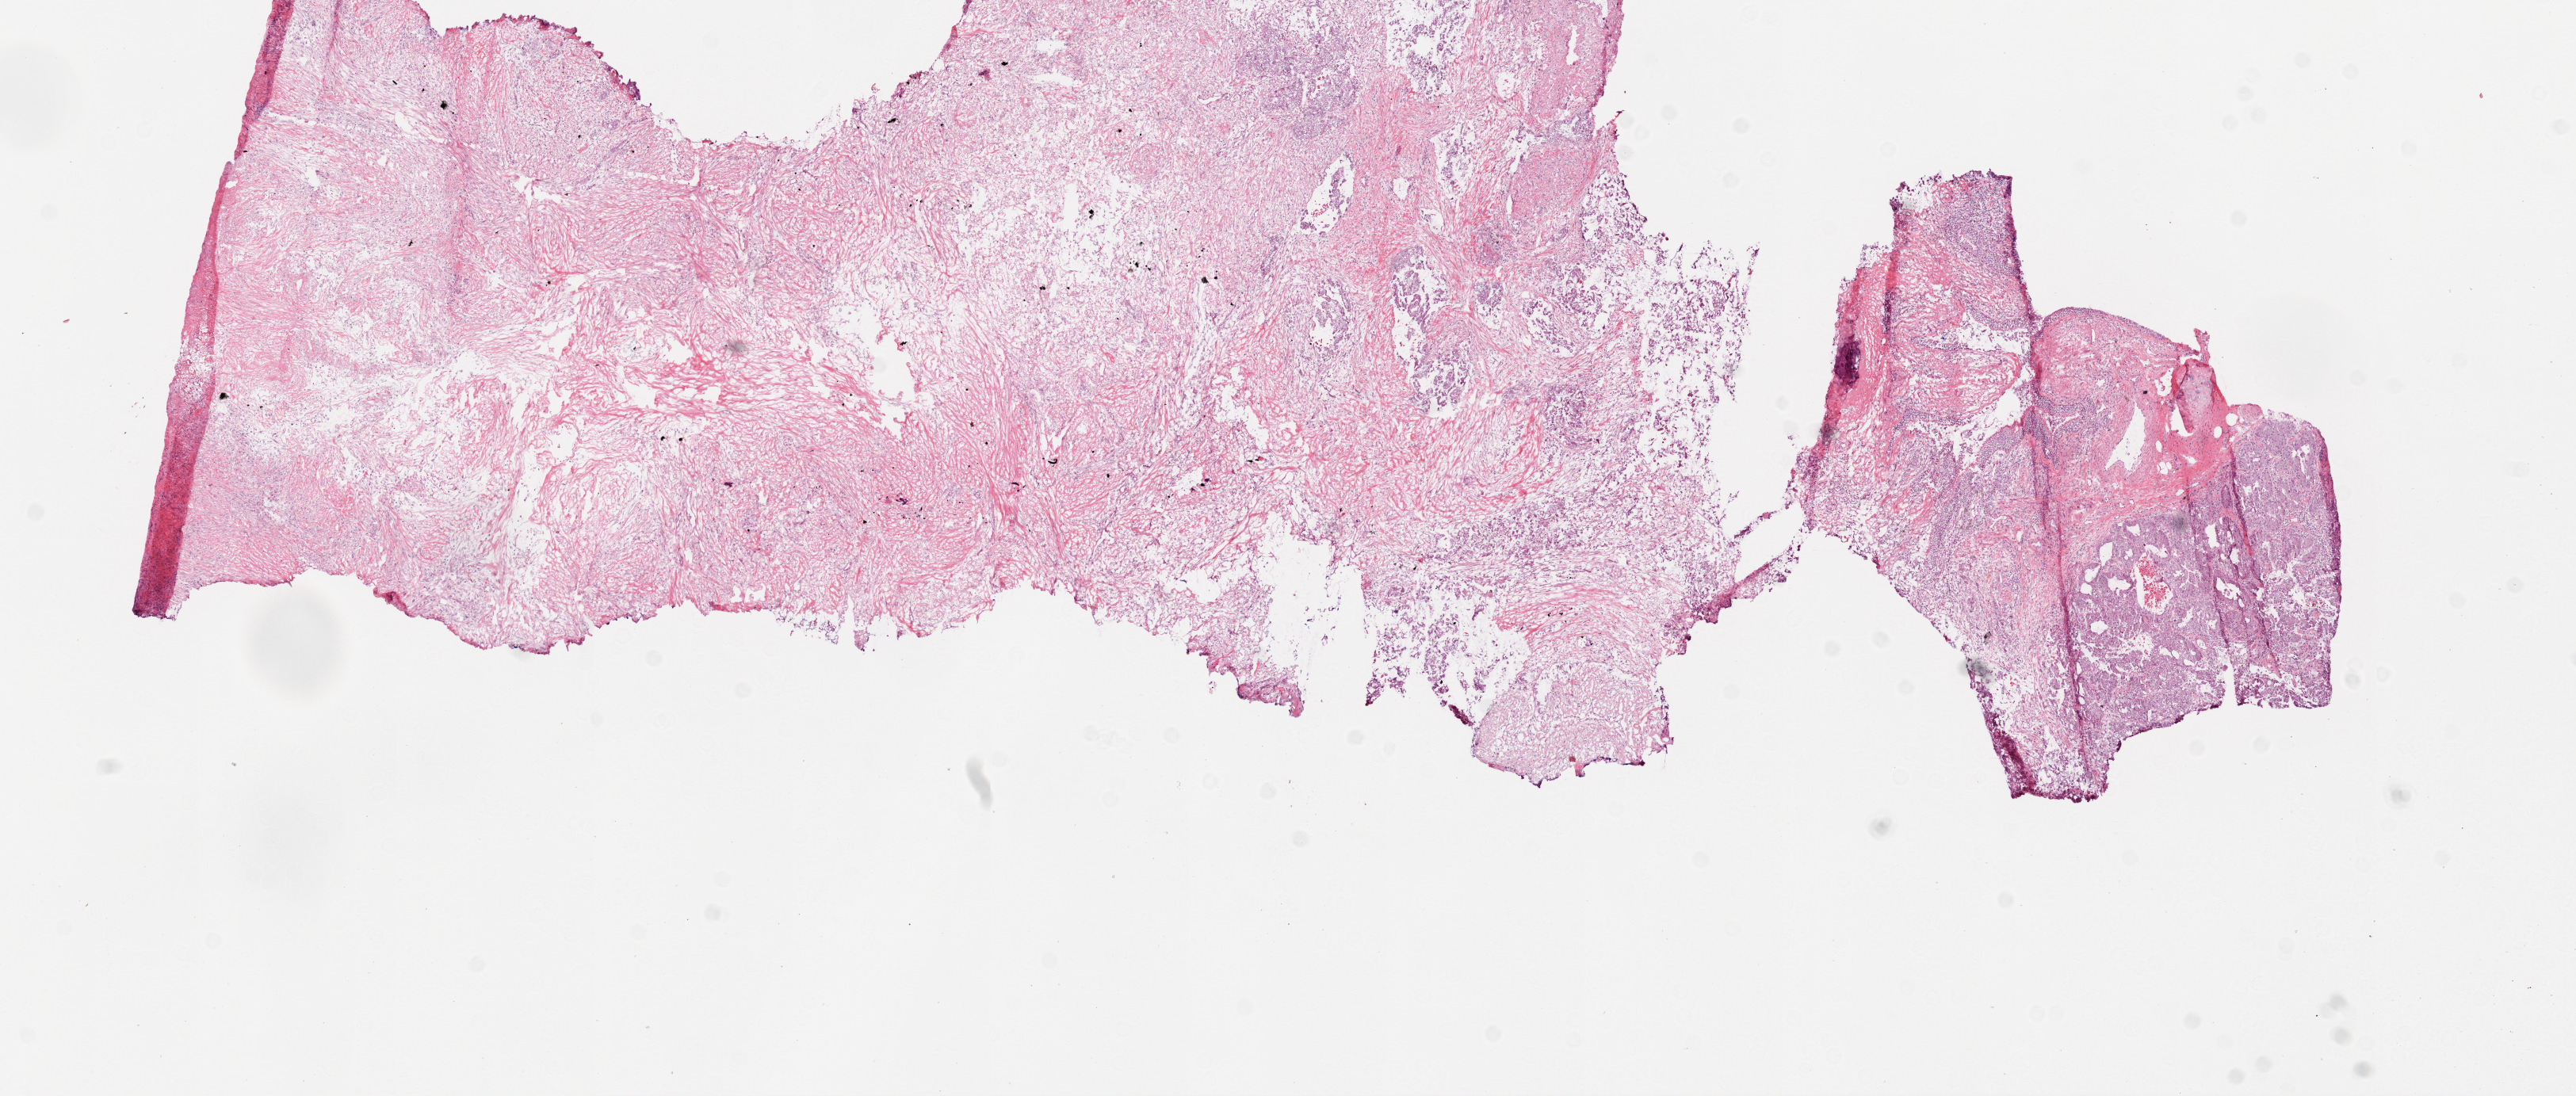
Digitized H&E-stained tissue section (whole slide) — low-resolution overview of the scanned area, about 13.0 x 5.5 mm. Frozen section. Primary tumour sample from the lung. Female, age 64 years at initial diagnosis. Slide review estimates, as recorded: tumour cells 55%, tumour nuclei 70%, normal cells 2%, stromal cells 40%, necrosis 3%.
• AJCC pathologic stage: IIA
• histologic diagnosis: Adenocarcinoma, NOS (upper lobe, lung)